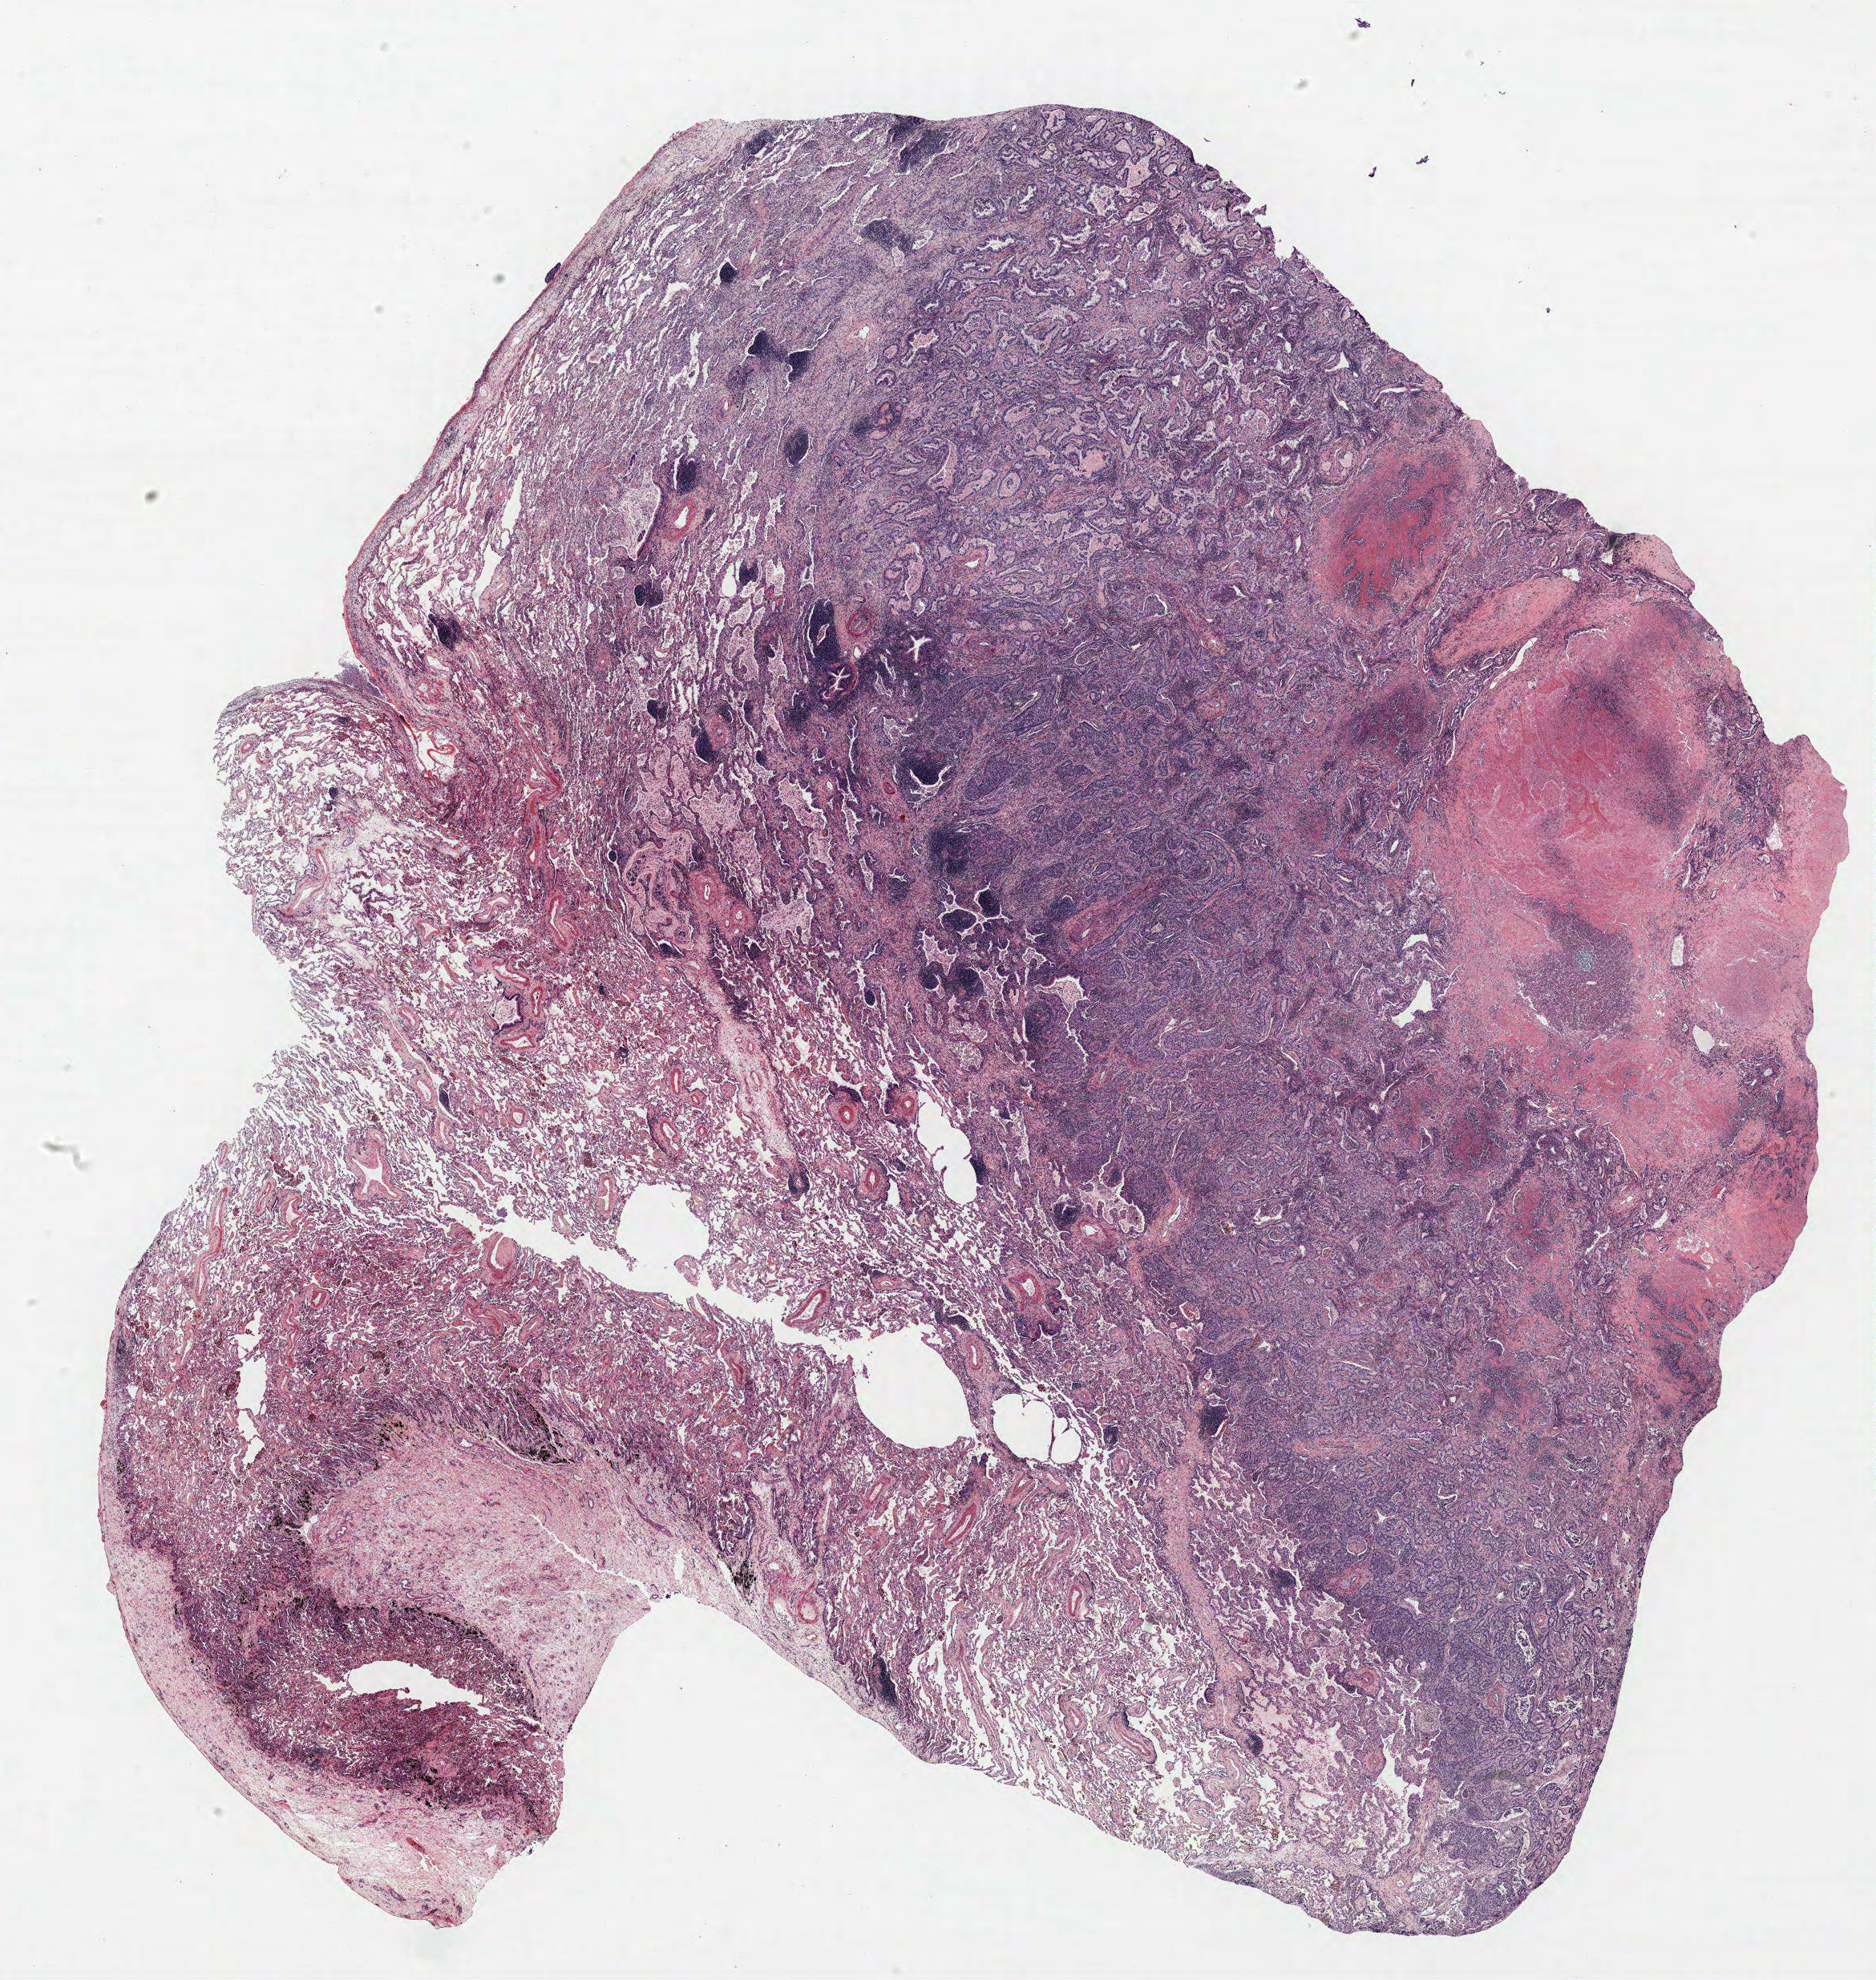
H&E whole-slide image — shown as a low-resolution overview of the whole scanned area (about 18.7 x 19.8 mm, acquisition: 40x scan); formalin-fixed paraffin-embedded (FFPE) section; lung. Male patient, aged 62 at enrolment. Former smoker at enrolment. Grade: moderately differentiated (G2).
Tumour size (pathology): 58 mm. Participant's lung-cancer diagnosis: Bronchiolo-alveolar adenocarcinoma, NOS (ICD-O-3 8250/3). Stage (AJCC 6th edition): IIIB. Primary tumour location (clinical record): left lower lobe.